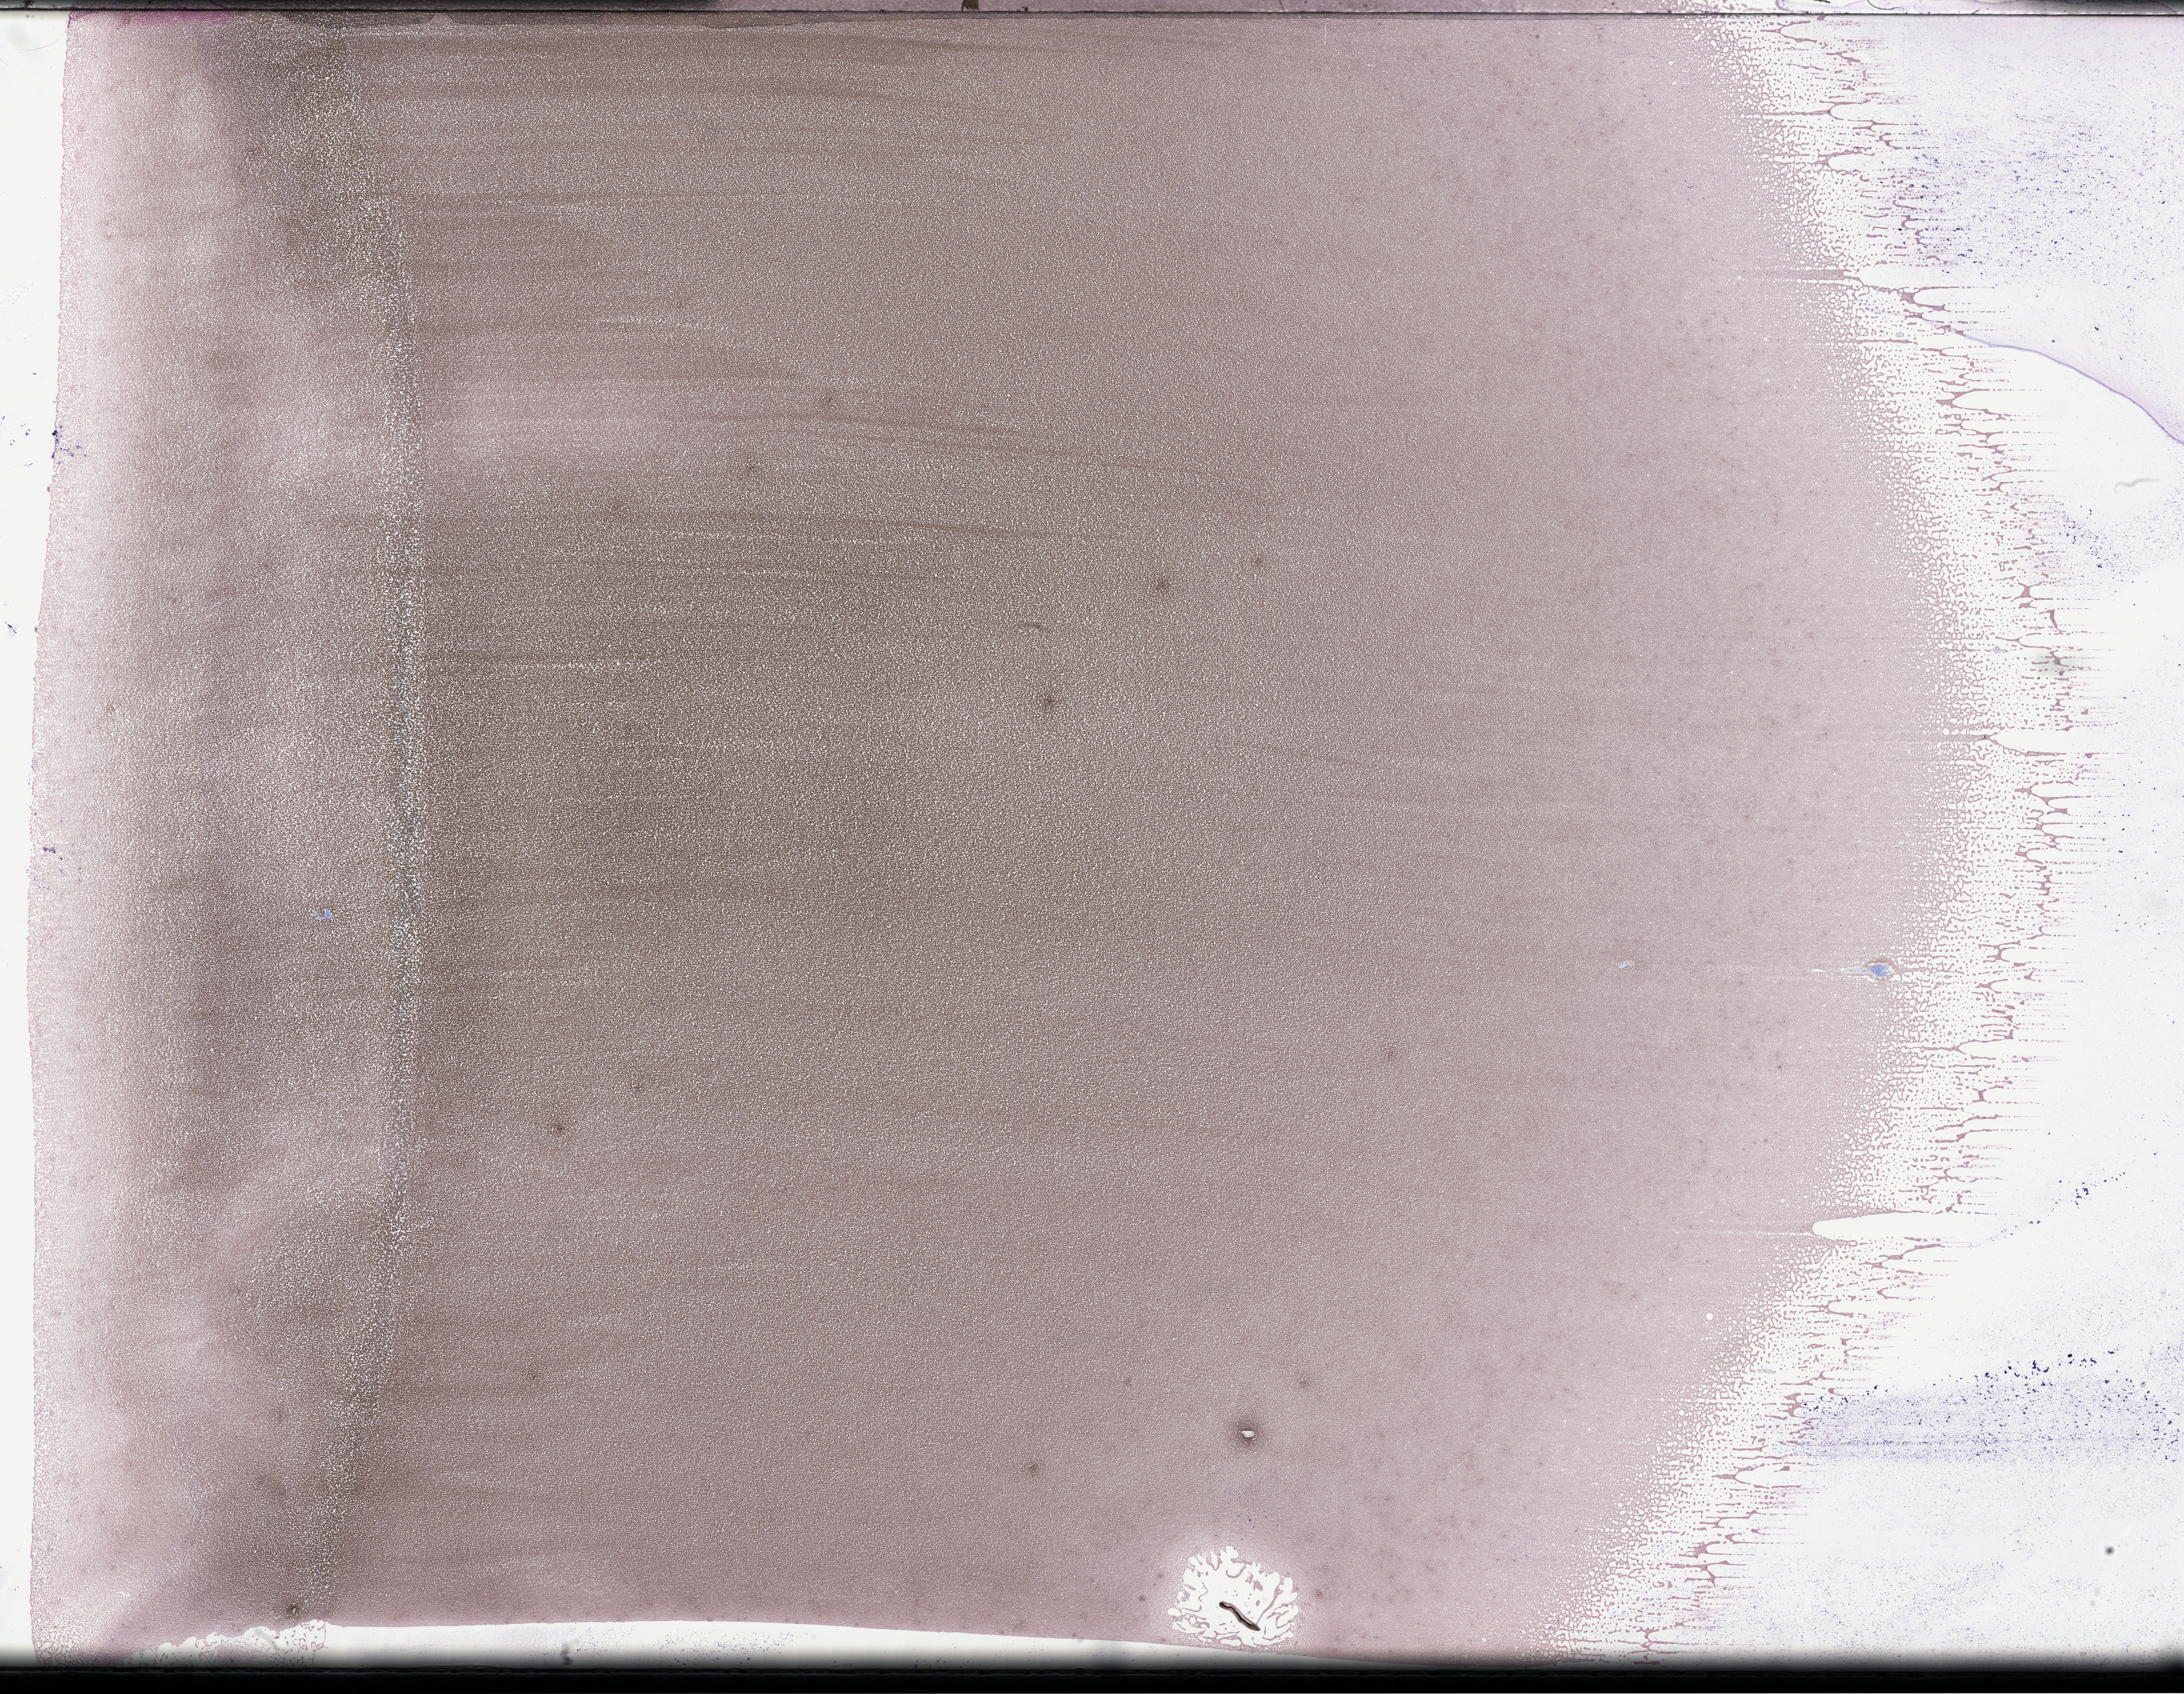
Whole-slide image of a whole blood smear, Wright–Giemsa stain, low-resolution overview of the scanned area, about 31.7 x 24.6 mm; EDTA-anticoagulated smear. Patient: male.
• patient diagnosis: Plasma Cell Myeloma